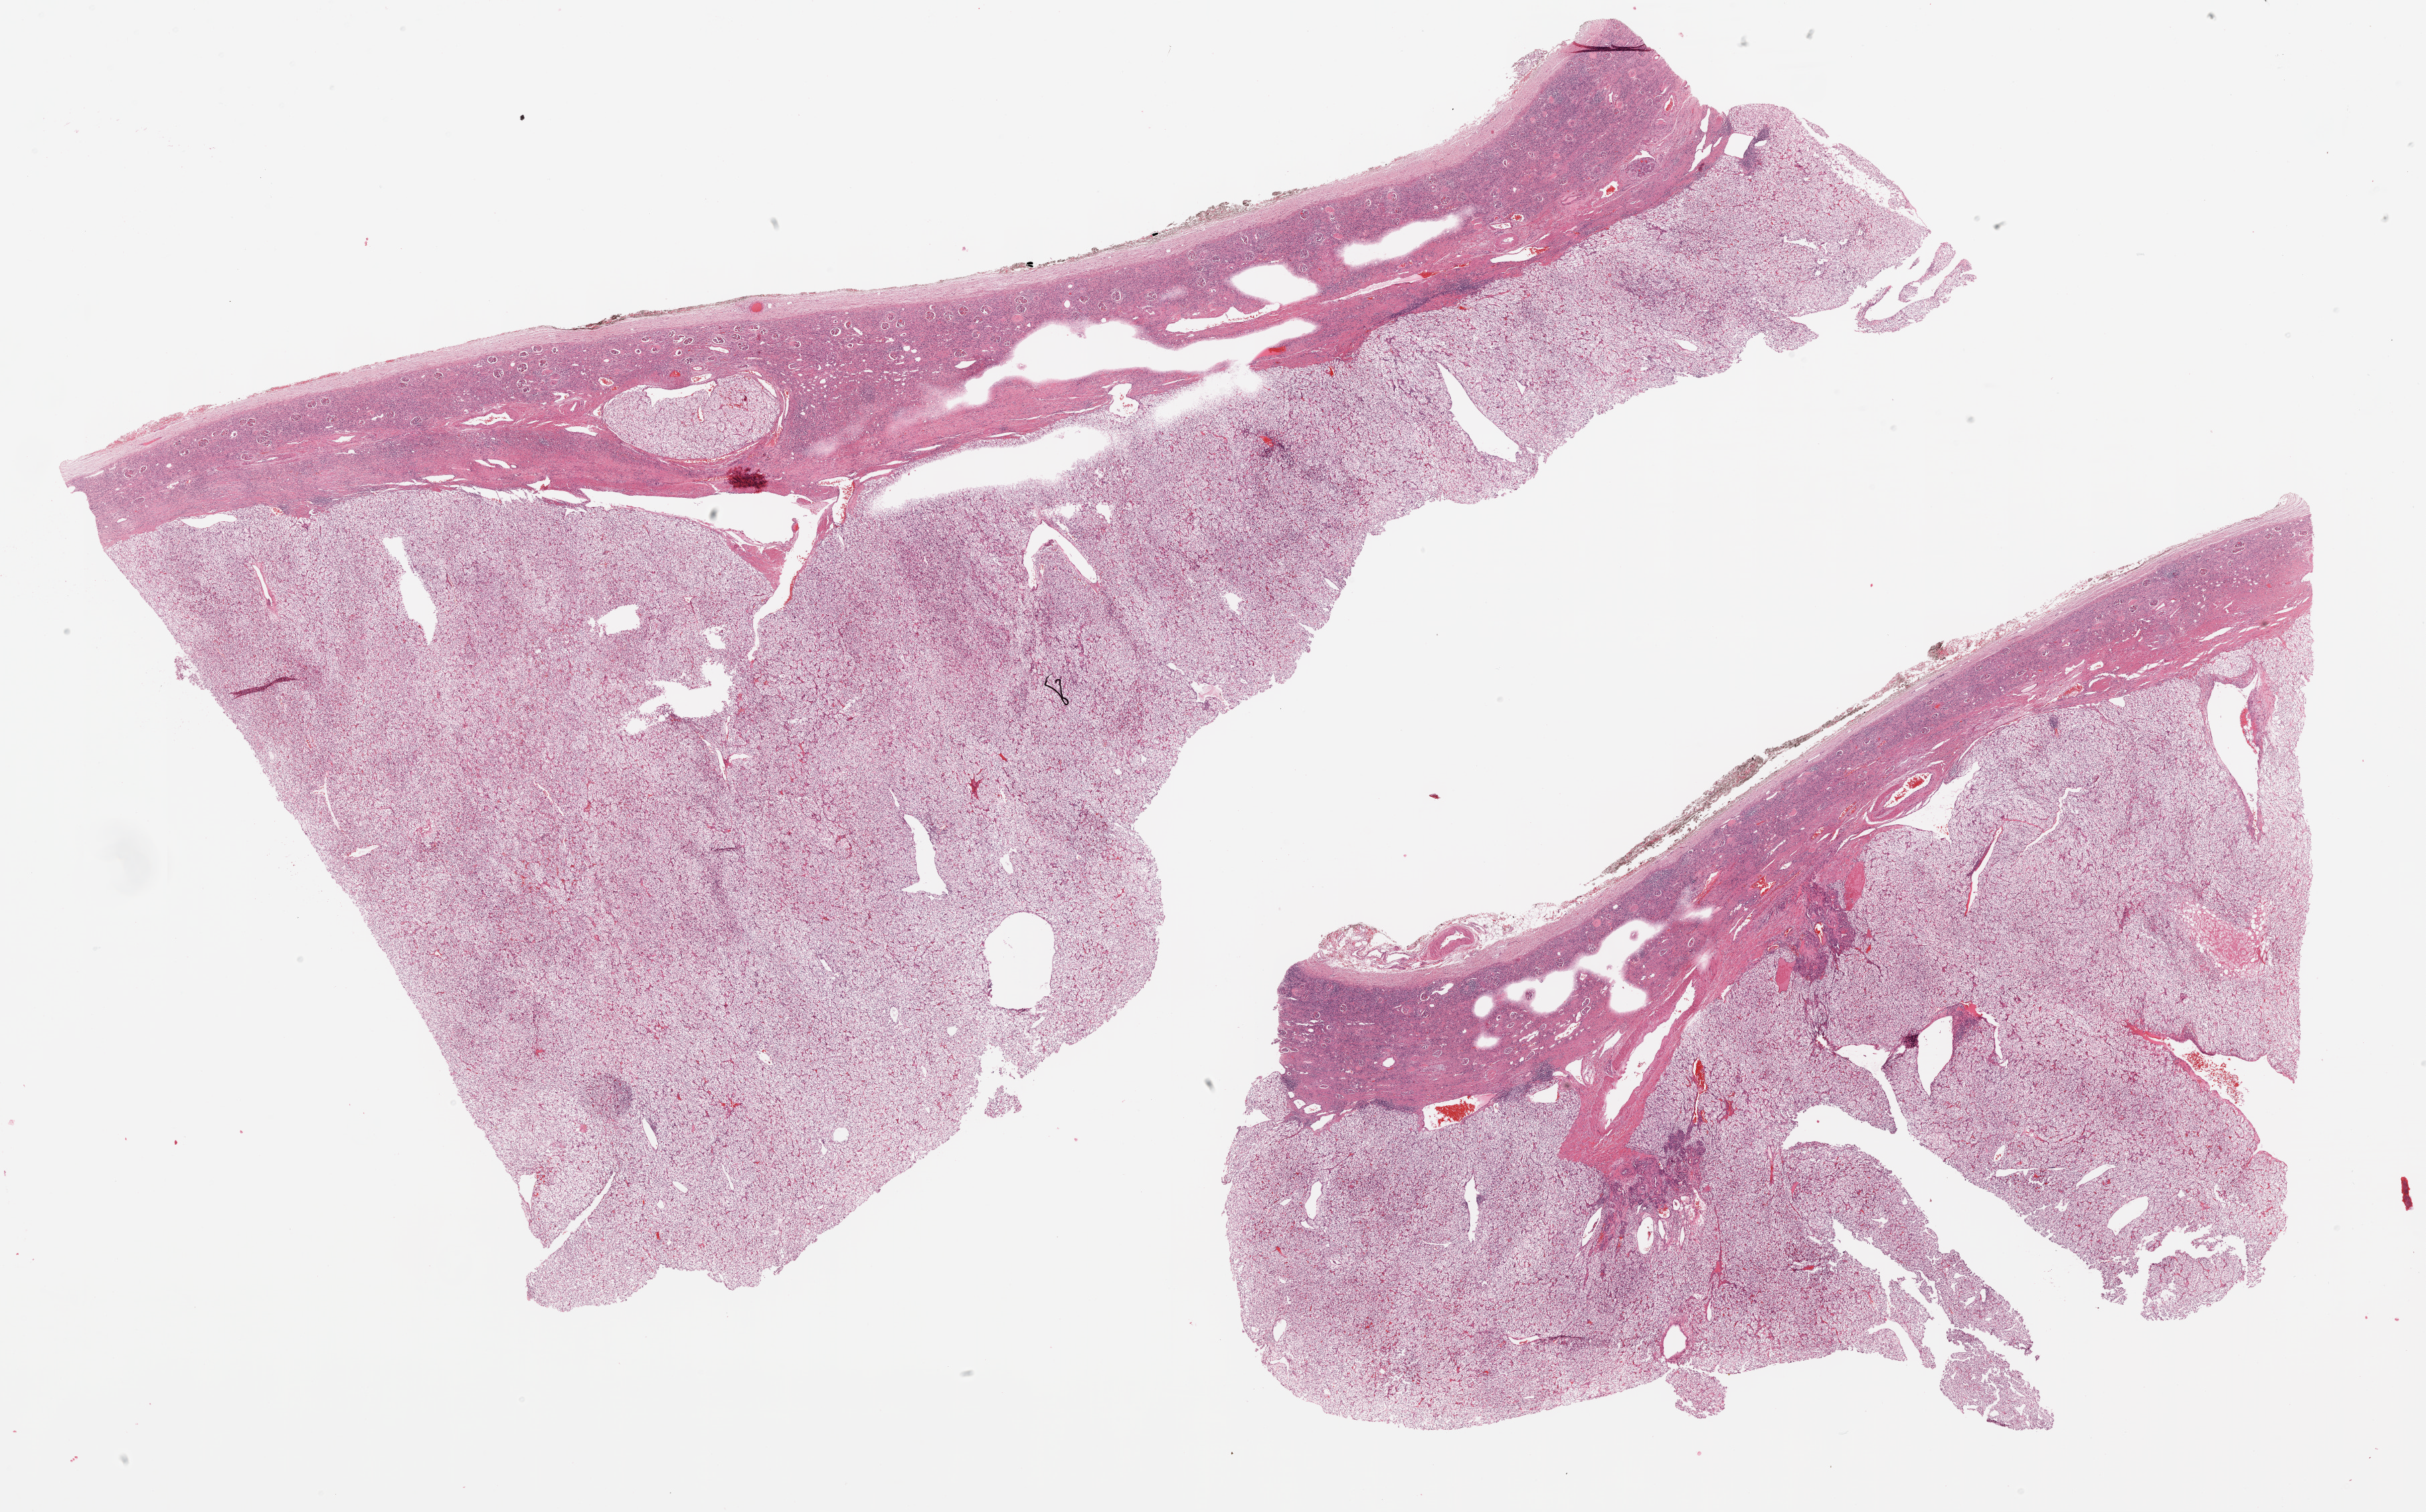
Digitized H&E tissue section (whole slide), a low-resolution overview of the entire scanned area, about 29.1 x 18.1 mm; formalin-fixed paraffin-embedded (FFPE) diagnostic section; kidney, primary tumour sample. Female patient; age at initial diagnosis 59 years. Histologic grade: G2 (moderately differentiated).
AJCC pathologic stage: I. Pathologic diagnosis: Clear cell adenocarcinoma, NOS.